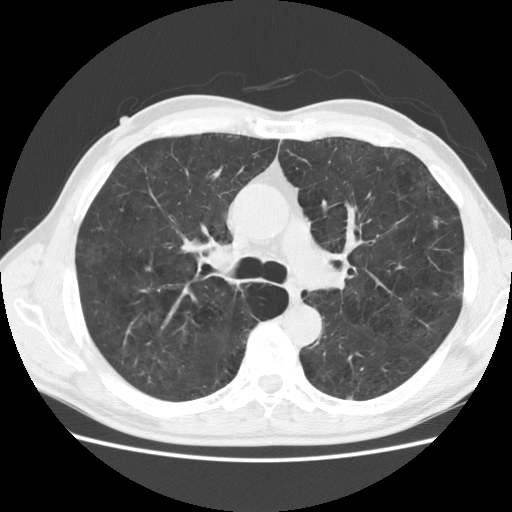
Low-dose screening chest CT, axial slice, first (baseline) screen, lung window (W 1500 / L -600 HU), 2.5 mm slice thickness, slice 69 of 177 in the series. Male, age 58 years at enrolment. Current smoker at enrolment.
- Expert-annotated lung lesion, bounding box <418,207,456,239> (left, top, right, bottom; pixels).
- No non-calcified nodule or mass ≥4 mm was recorded by the screening reader at this exam.
- Official screen result: negative screen, minor abnormalities not suspicious for lung cancer.
- Participant outcome: lung cancer diagnosed 832 days after this screen — adenocarcinoma, NOS, left upper lobe, stage IA (AJCC 6th edition), 9 mm at pathology.